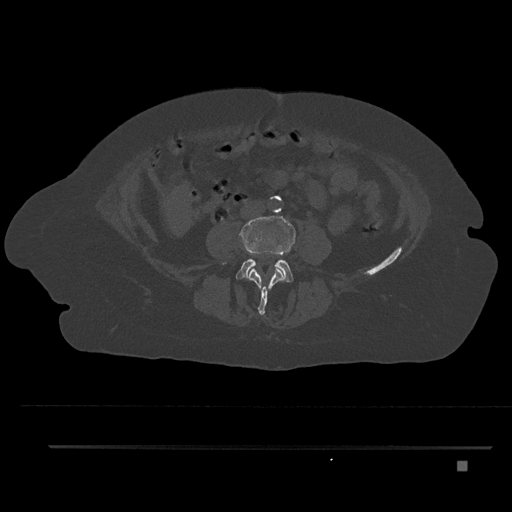
CT including the spine, one axial slice; slice 99 of 797 in the series (ordered by position); bone window (W 1800 / L 400 HU); 0.5 mm slice thickness; 512 × 512 image matrix, field of view 437 × 437 mm. Female patient, age 76 years. Case-level facts recorded for this patient, not image findings: primary cancer: lung; vertebrae with lytic lesions (as recorded): T11, L3.
Annotated regions visible in this slice (semi-automatically segmented with operator editing):
- L3 vertebra: bounding box <248,217,285,315> (left, top, right, bottom; pixels)
- L4 vertebra: <235,216,296,283>